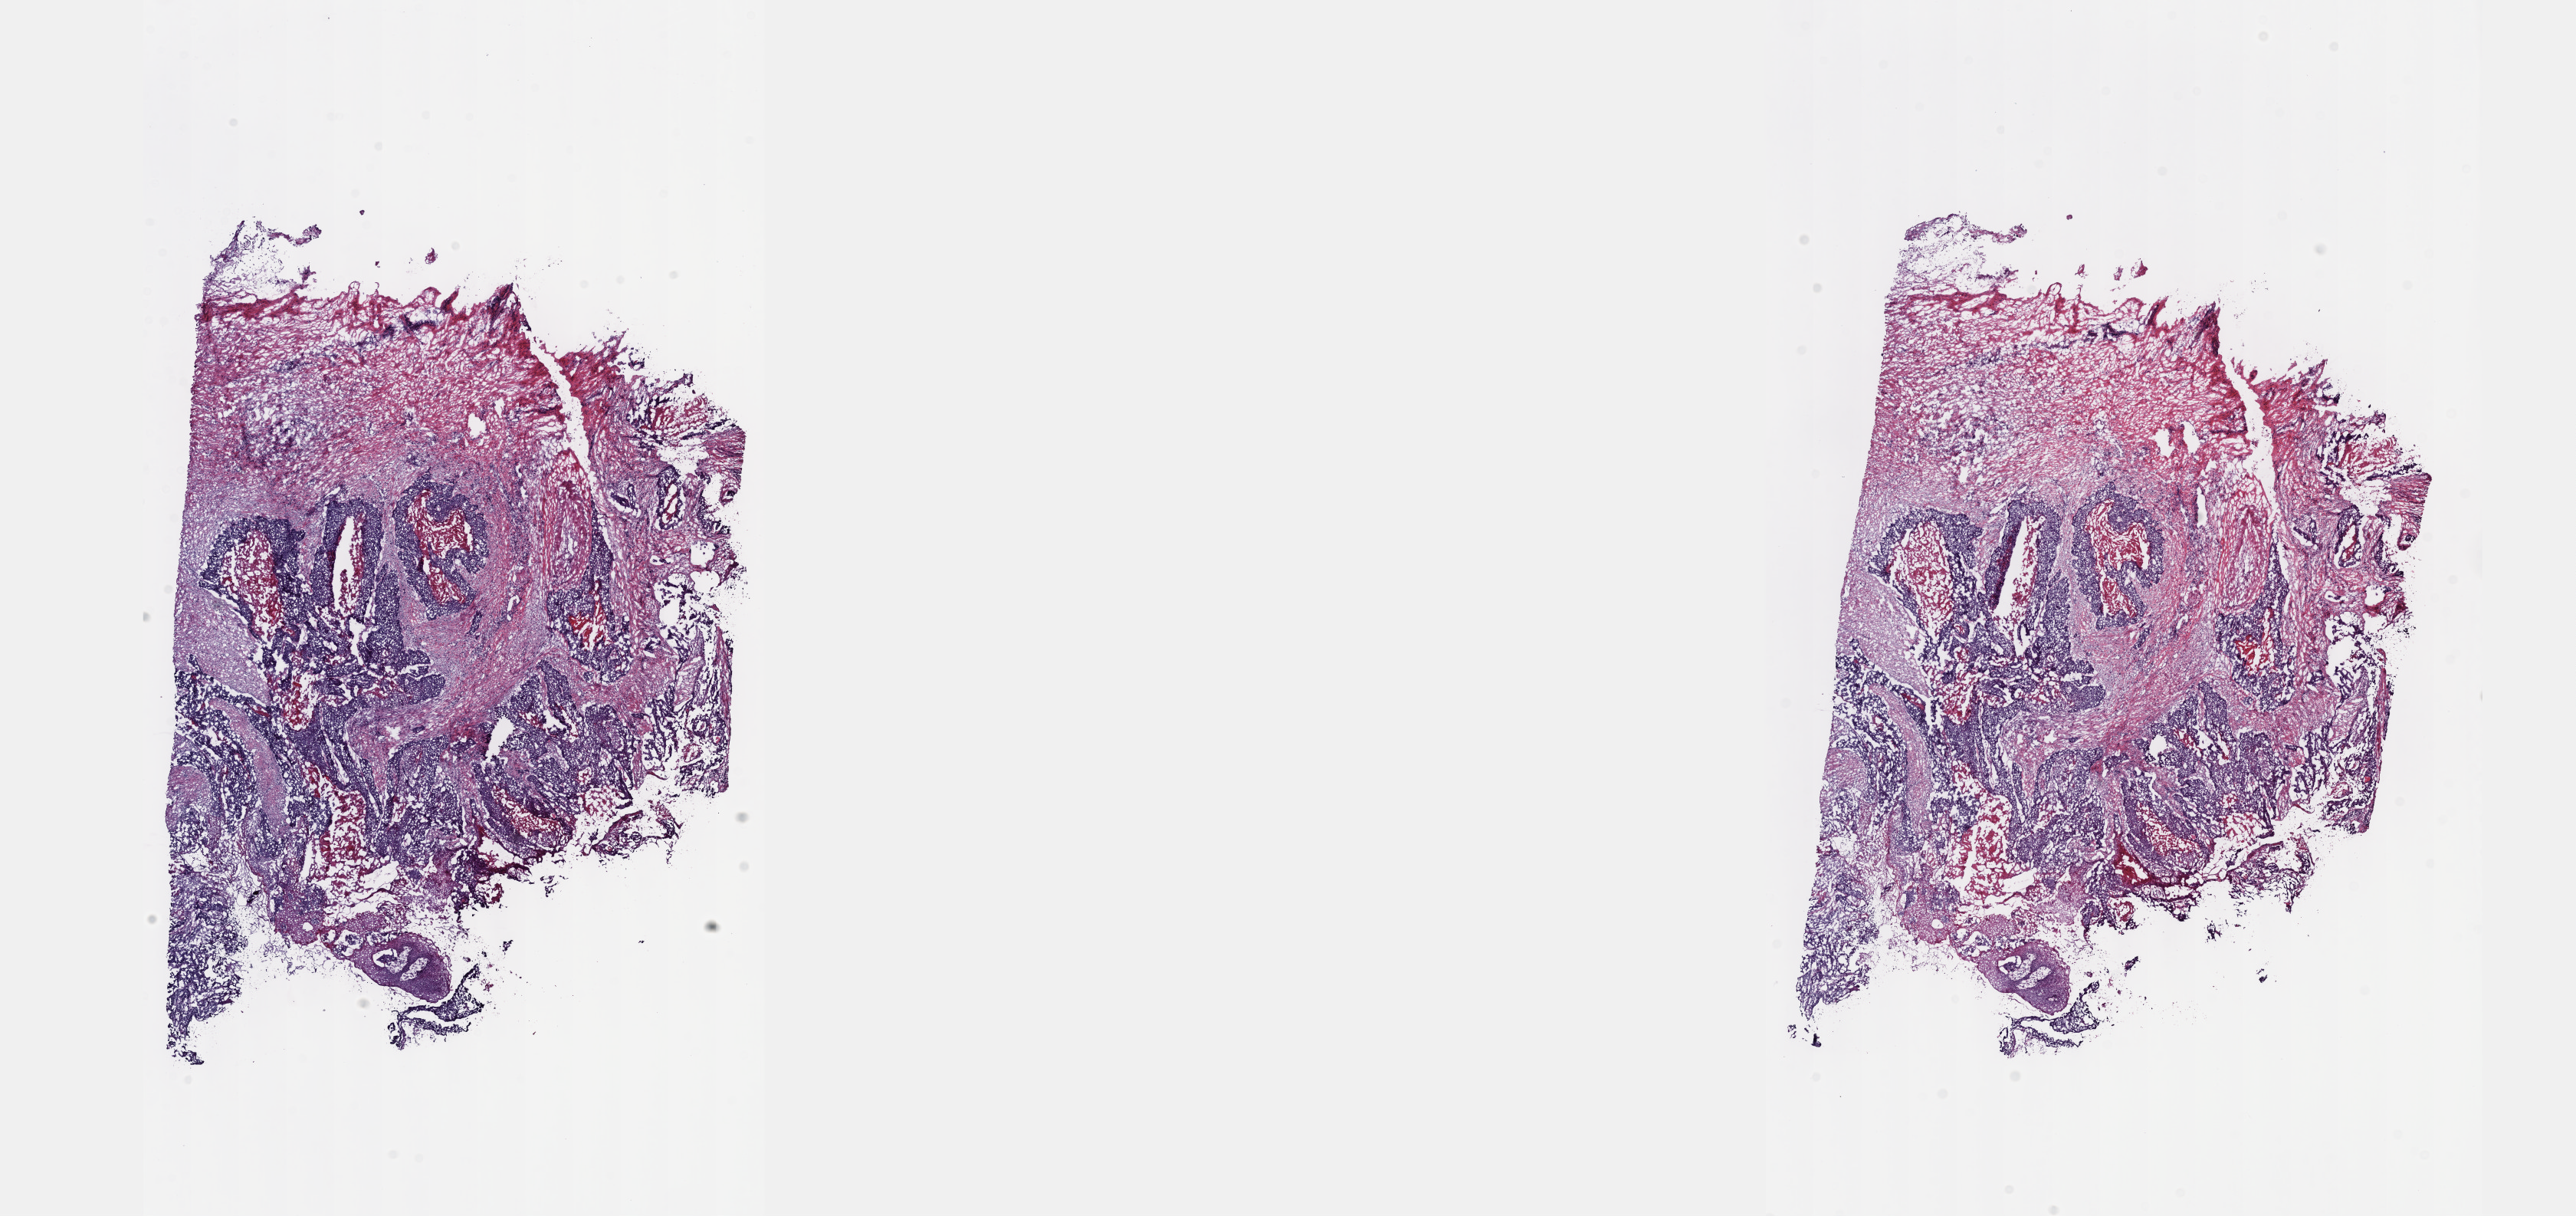
Digitized H&E-stained tissue section (whole slide) — a low-resolution overview of the entire scanned area, about 27.2 x 12.8 mm (slide scanned at 40x), frozen section from the top of the tissue portion, head and neck, primary tumour sample. Male, age 59 years at initial diagnosis. Composition of this section per pathologist review: tumour cells 70%, tumour nuclei 70%, normal cells 0%, stromal cells 30%, necrosis 0%. Inflammatory infiltration, as recorded: lymphocyte infiltration 10%, monocyte infiltration 0%, neutrophil infiltration 0%.
* histologic diagnosis: Basaloid squamous cell carcinoma
* laterality: left
* AJCC pathologic stage: IVA (7th edition)